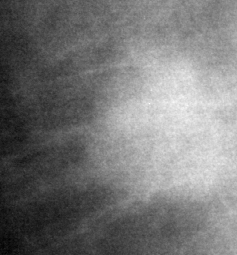
Cropped region of a digitized screen-film mammogram centred on a radiologist-marked abnormality, right breast, MLO view, BI-RADS breast density category 2 (scale 1–4).
Finding: mass, shape round, margins microlobulated; BI-RADS assessment category 5; subtlety rating 5 on a 1 (subtle) to 5 (obvious) scale; pathology result (as recorded, not read from the image): malignant.